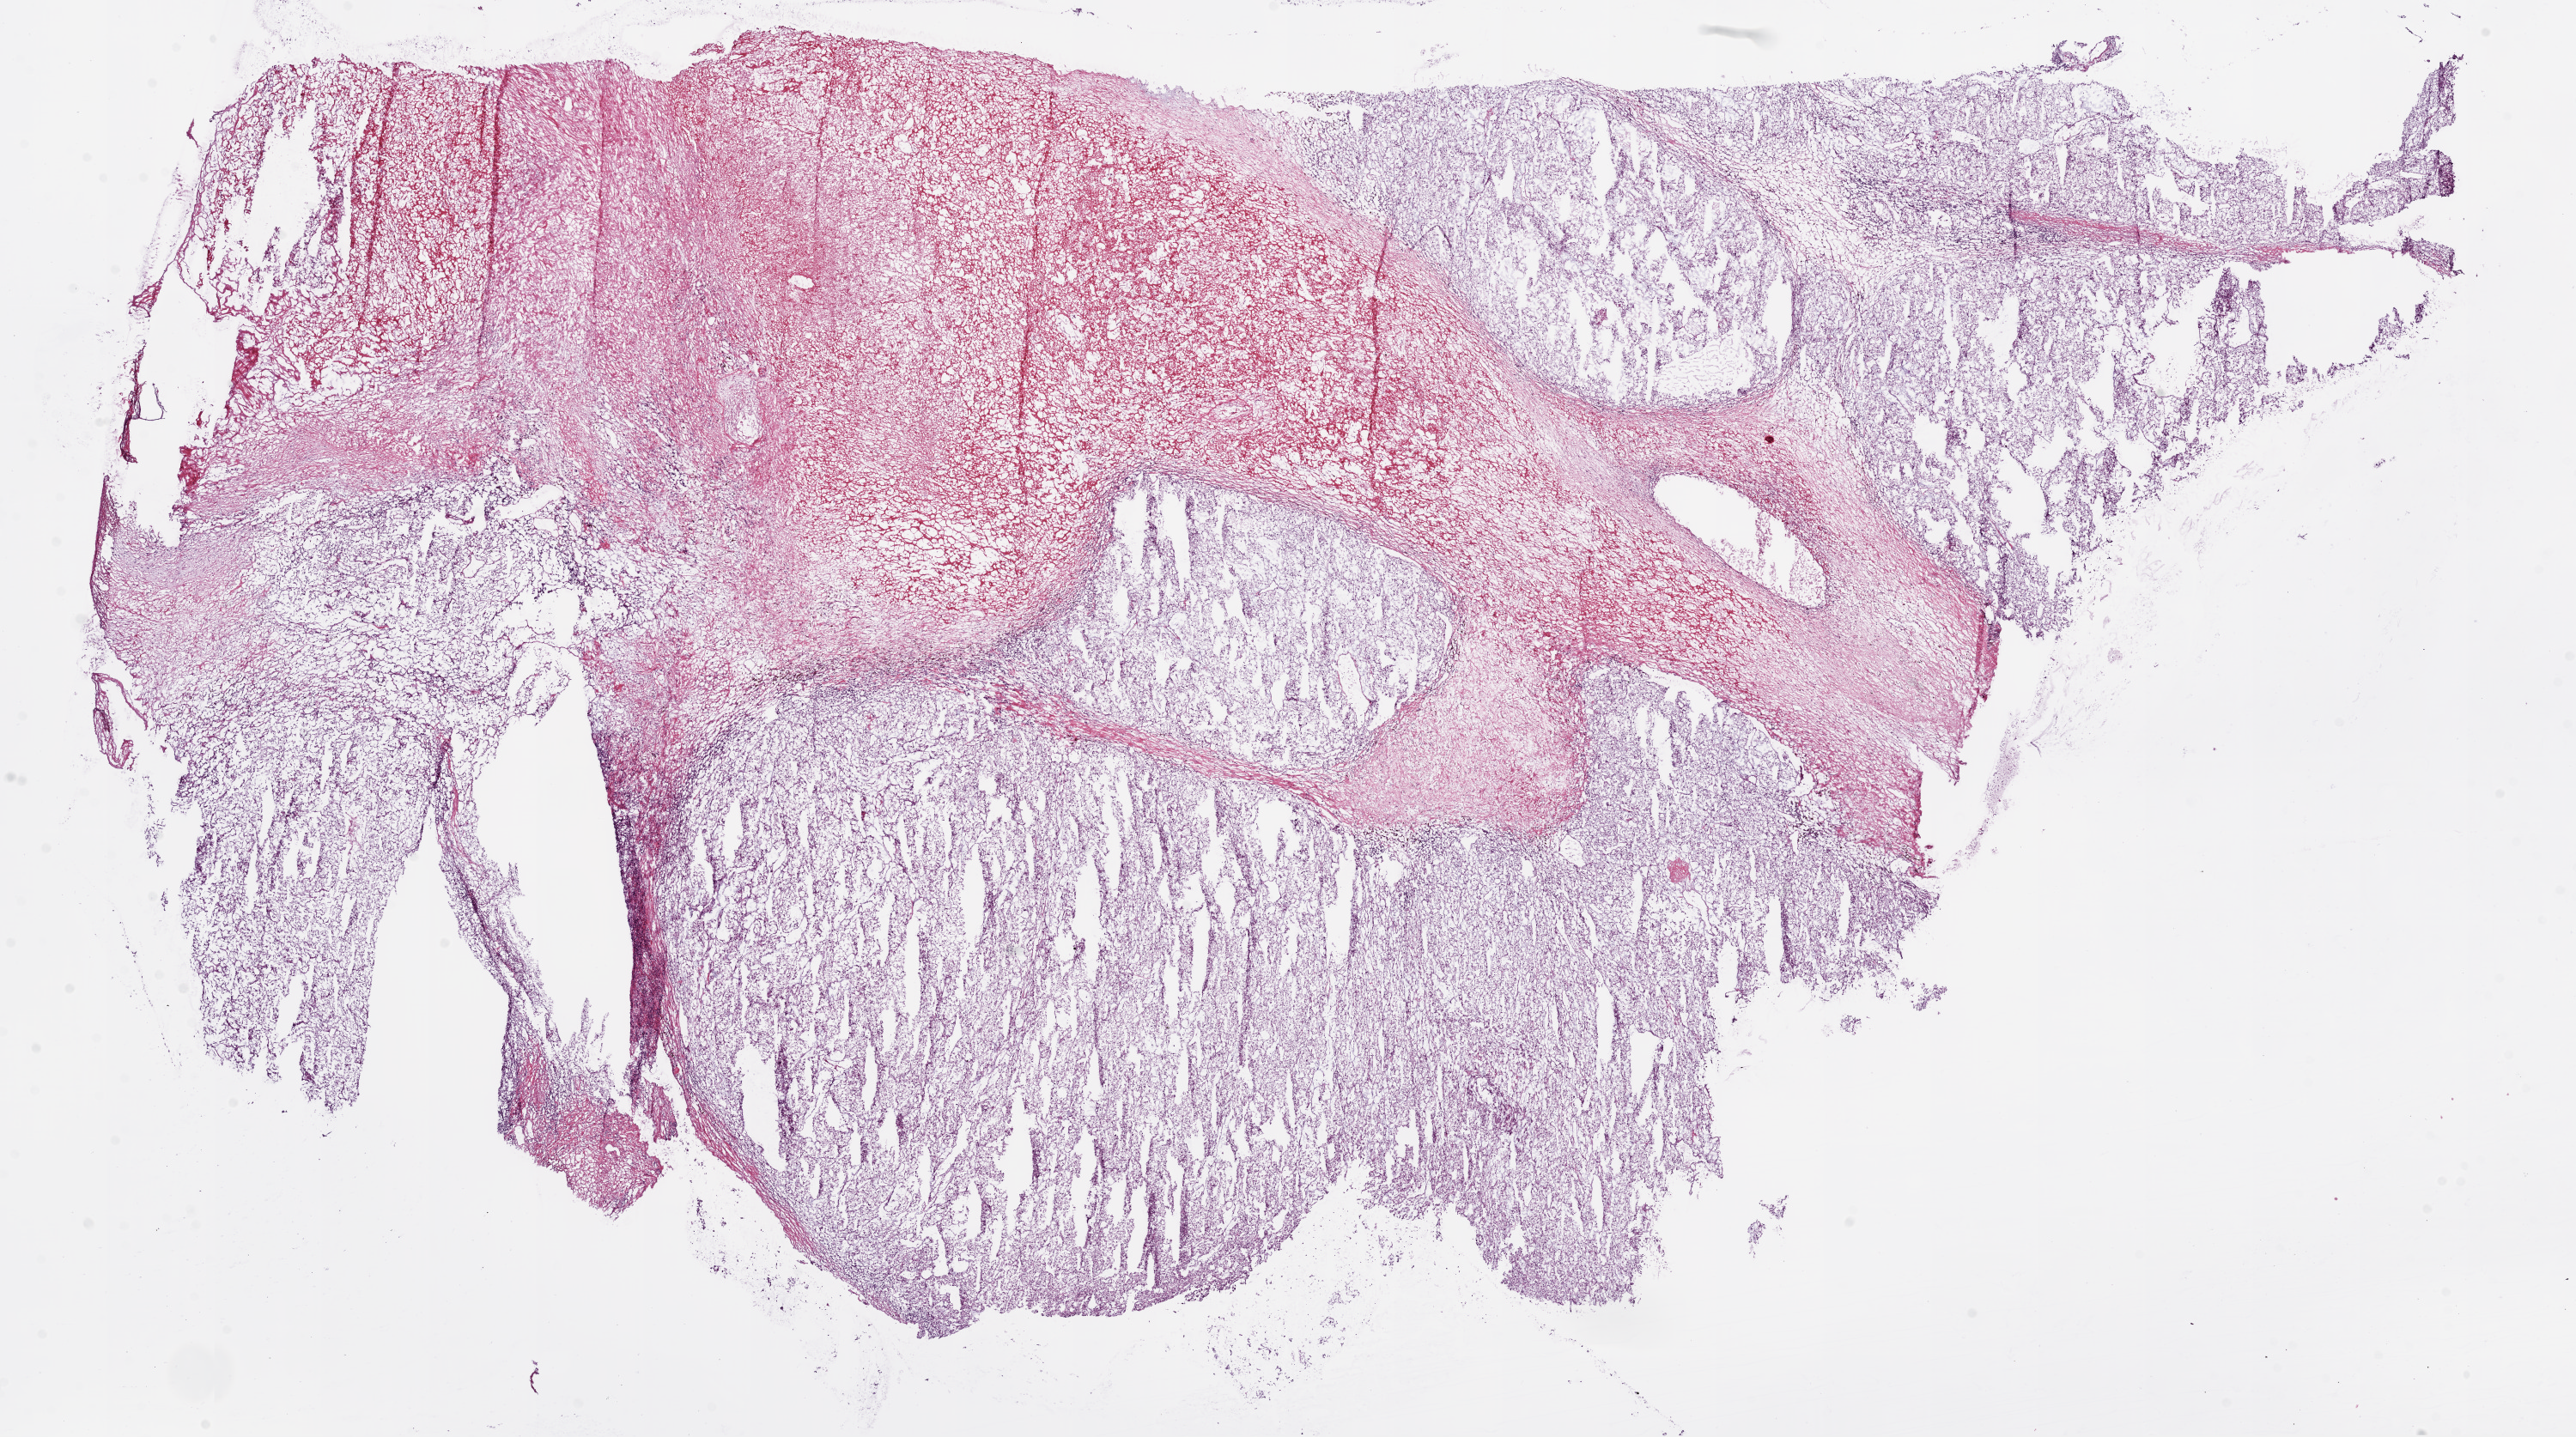
Hematoxylin and eosin (H&E) stained whole-slide image, low-resolution overview of the scanned area, about 24.1 x 13.4 mm (acquisition: 20x scan); frozen section from the bottom of the tissue portion; sample: primary tumour, kidney. Female patient; age at initial diagnosis 77 years. Histologic grade: G4 (undifferentiated). Slide review estimates, as recorded: tumour cells 70%, tumour nuclei 85%, normal cells 0%, stromal cells 30%, necrosis 0%.
Histologic diagnosis: Clear cell adenocarcinoma, NOS. AJCC pathologic stage: III.